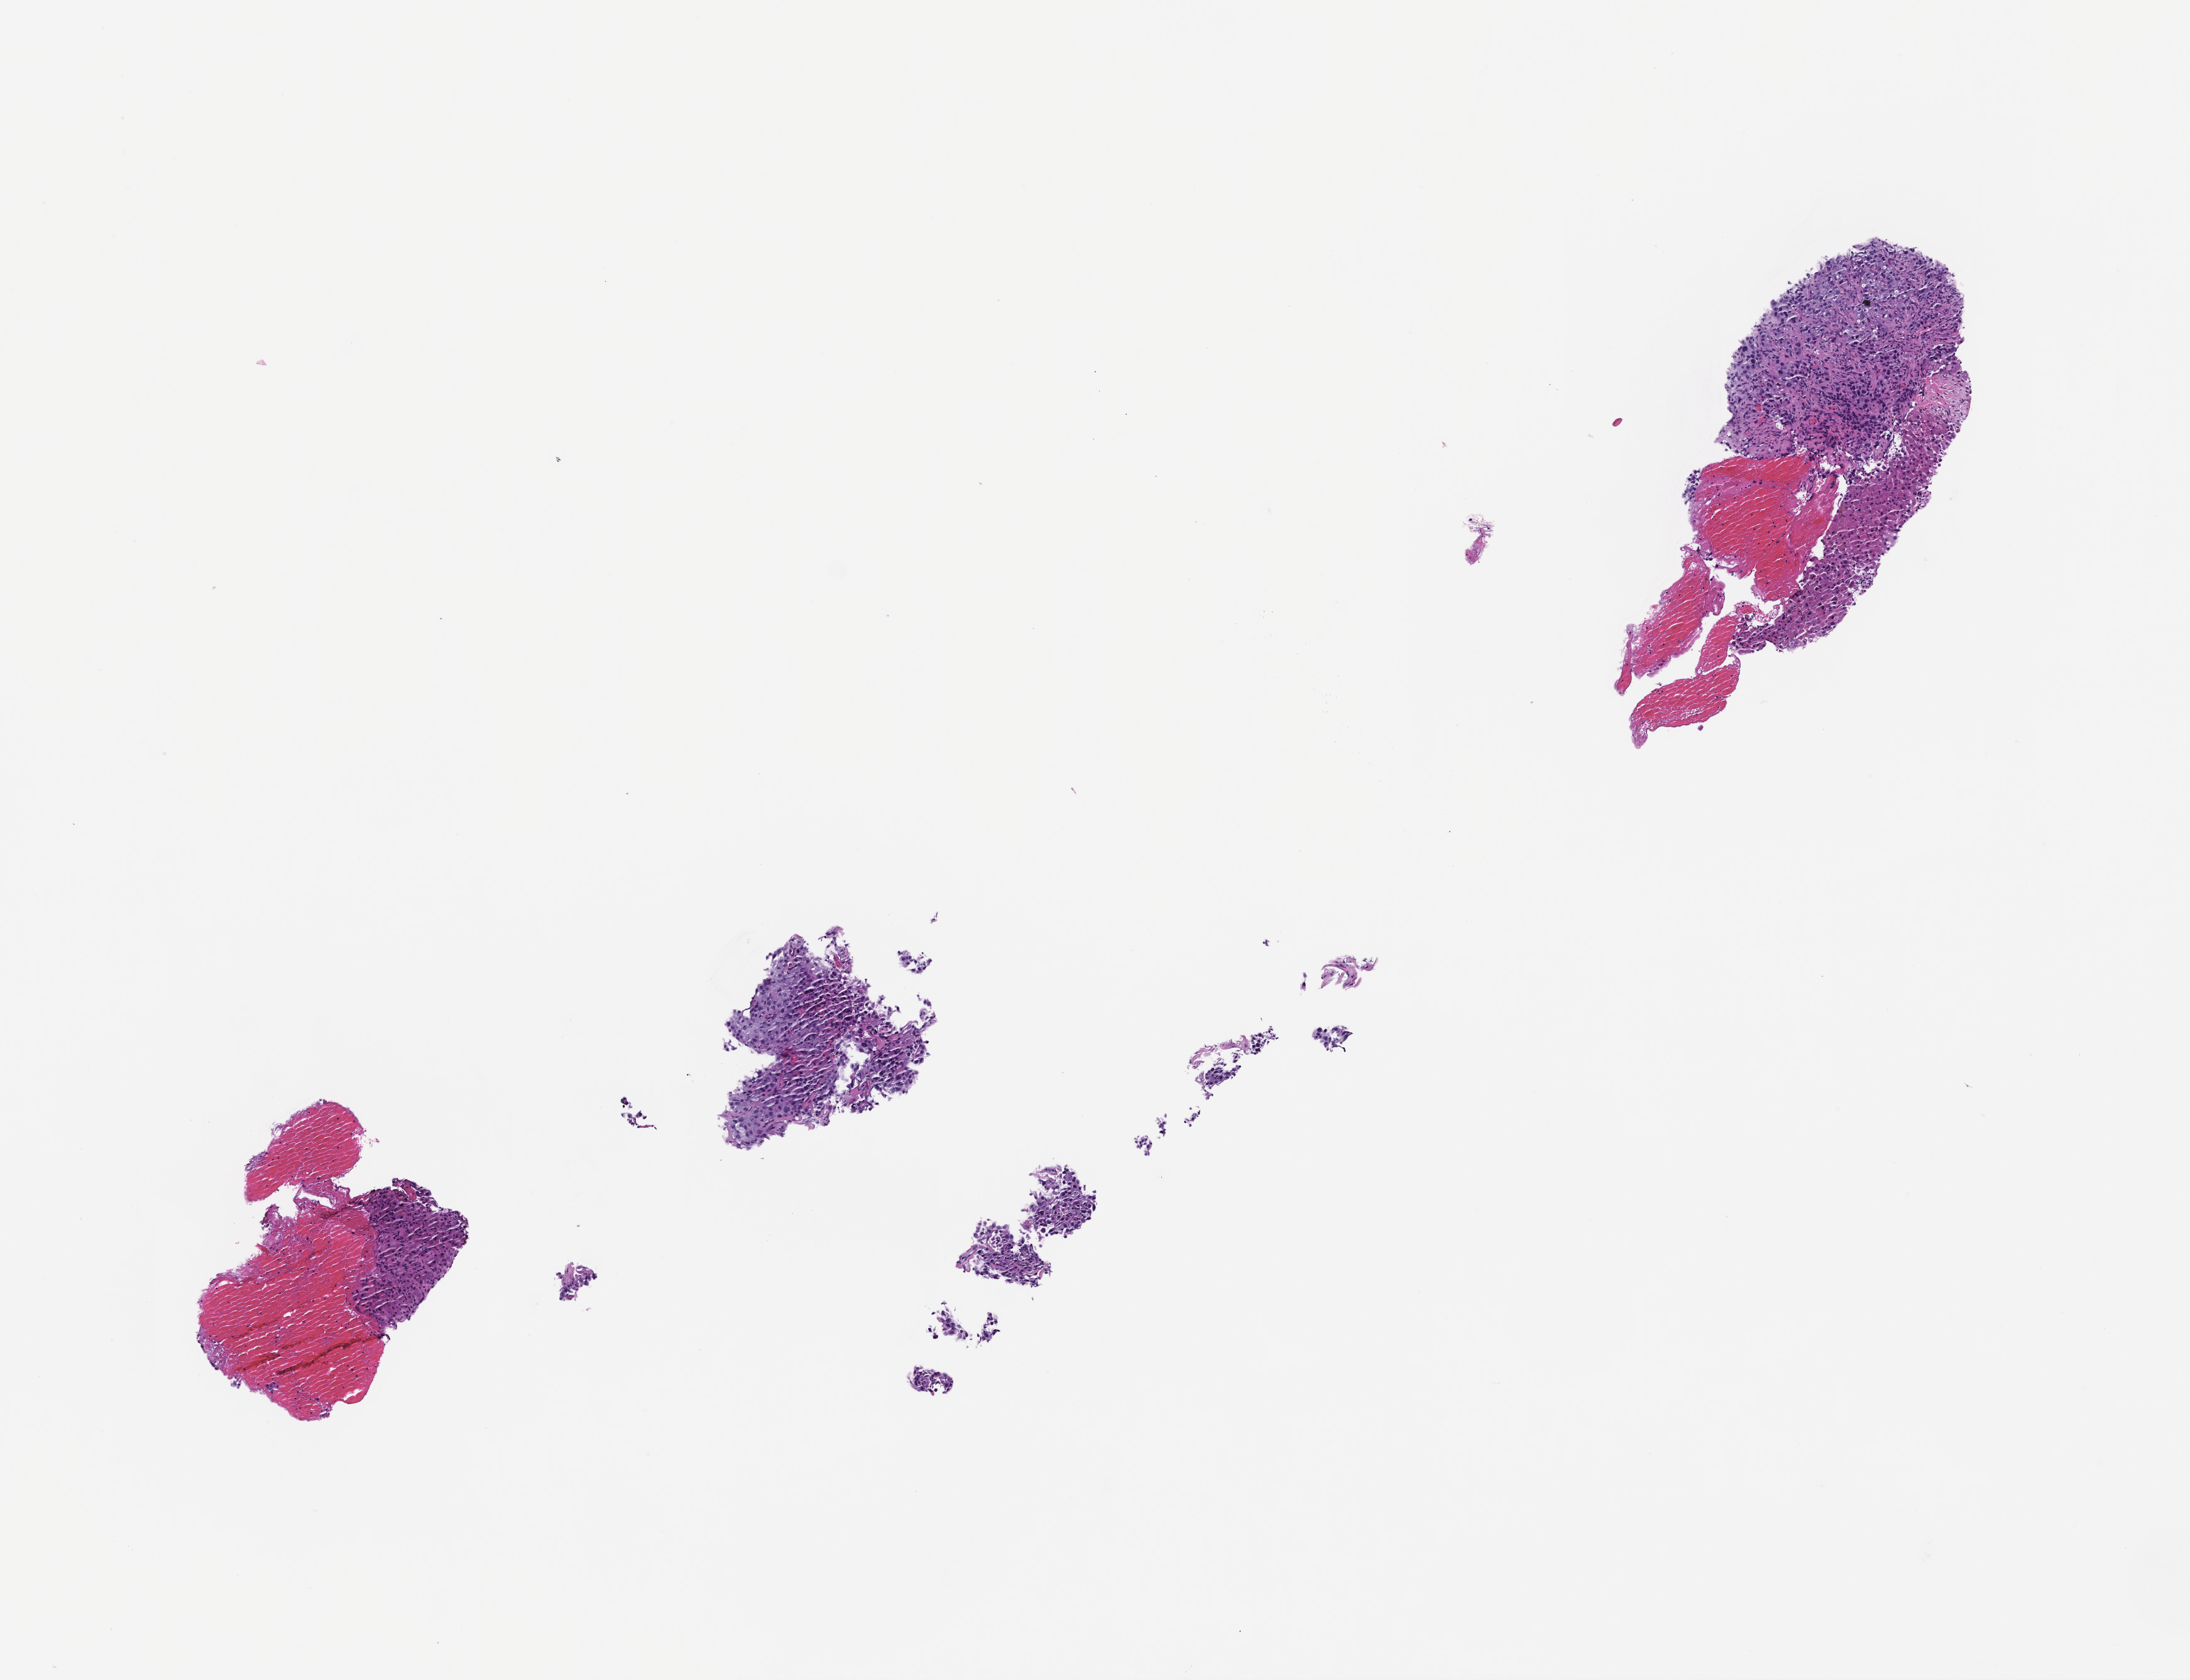
Digitized H&E-stained section — low-resolution overview of the scanned area, about 7.0 x 5.4 mm; formalin-fixed paraffin-embedded section. Patient: male.
- this section: metastasis (sampled organ not recorded)
- patient diagnosis (primary): Non-Small Cell Lung Carcinoma